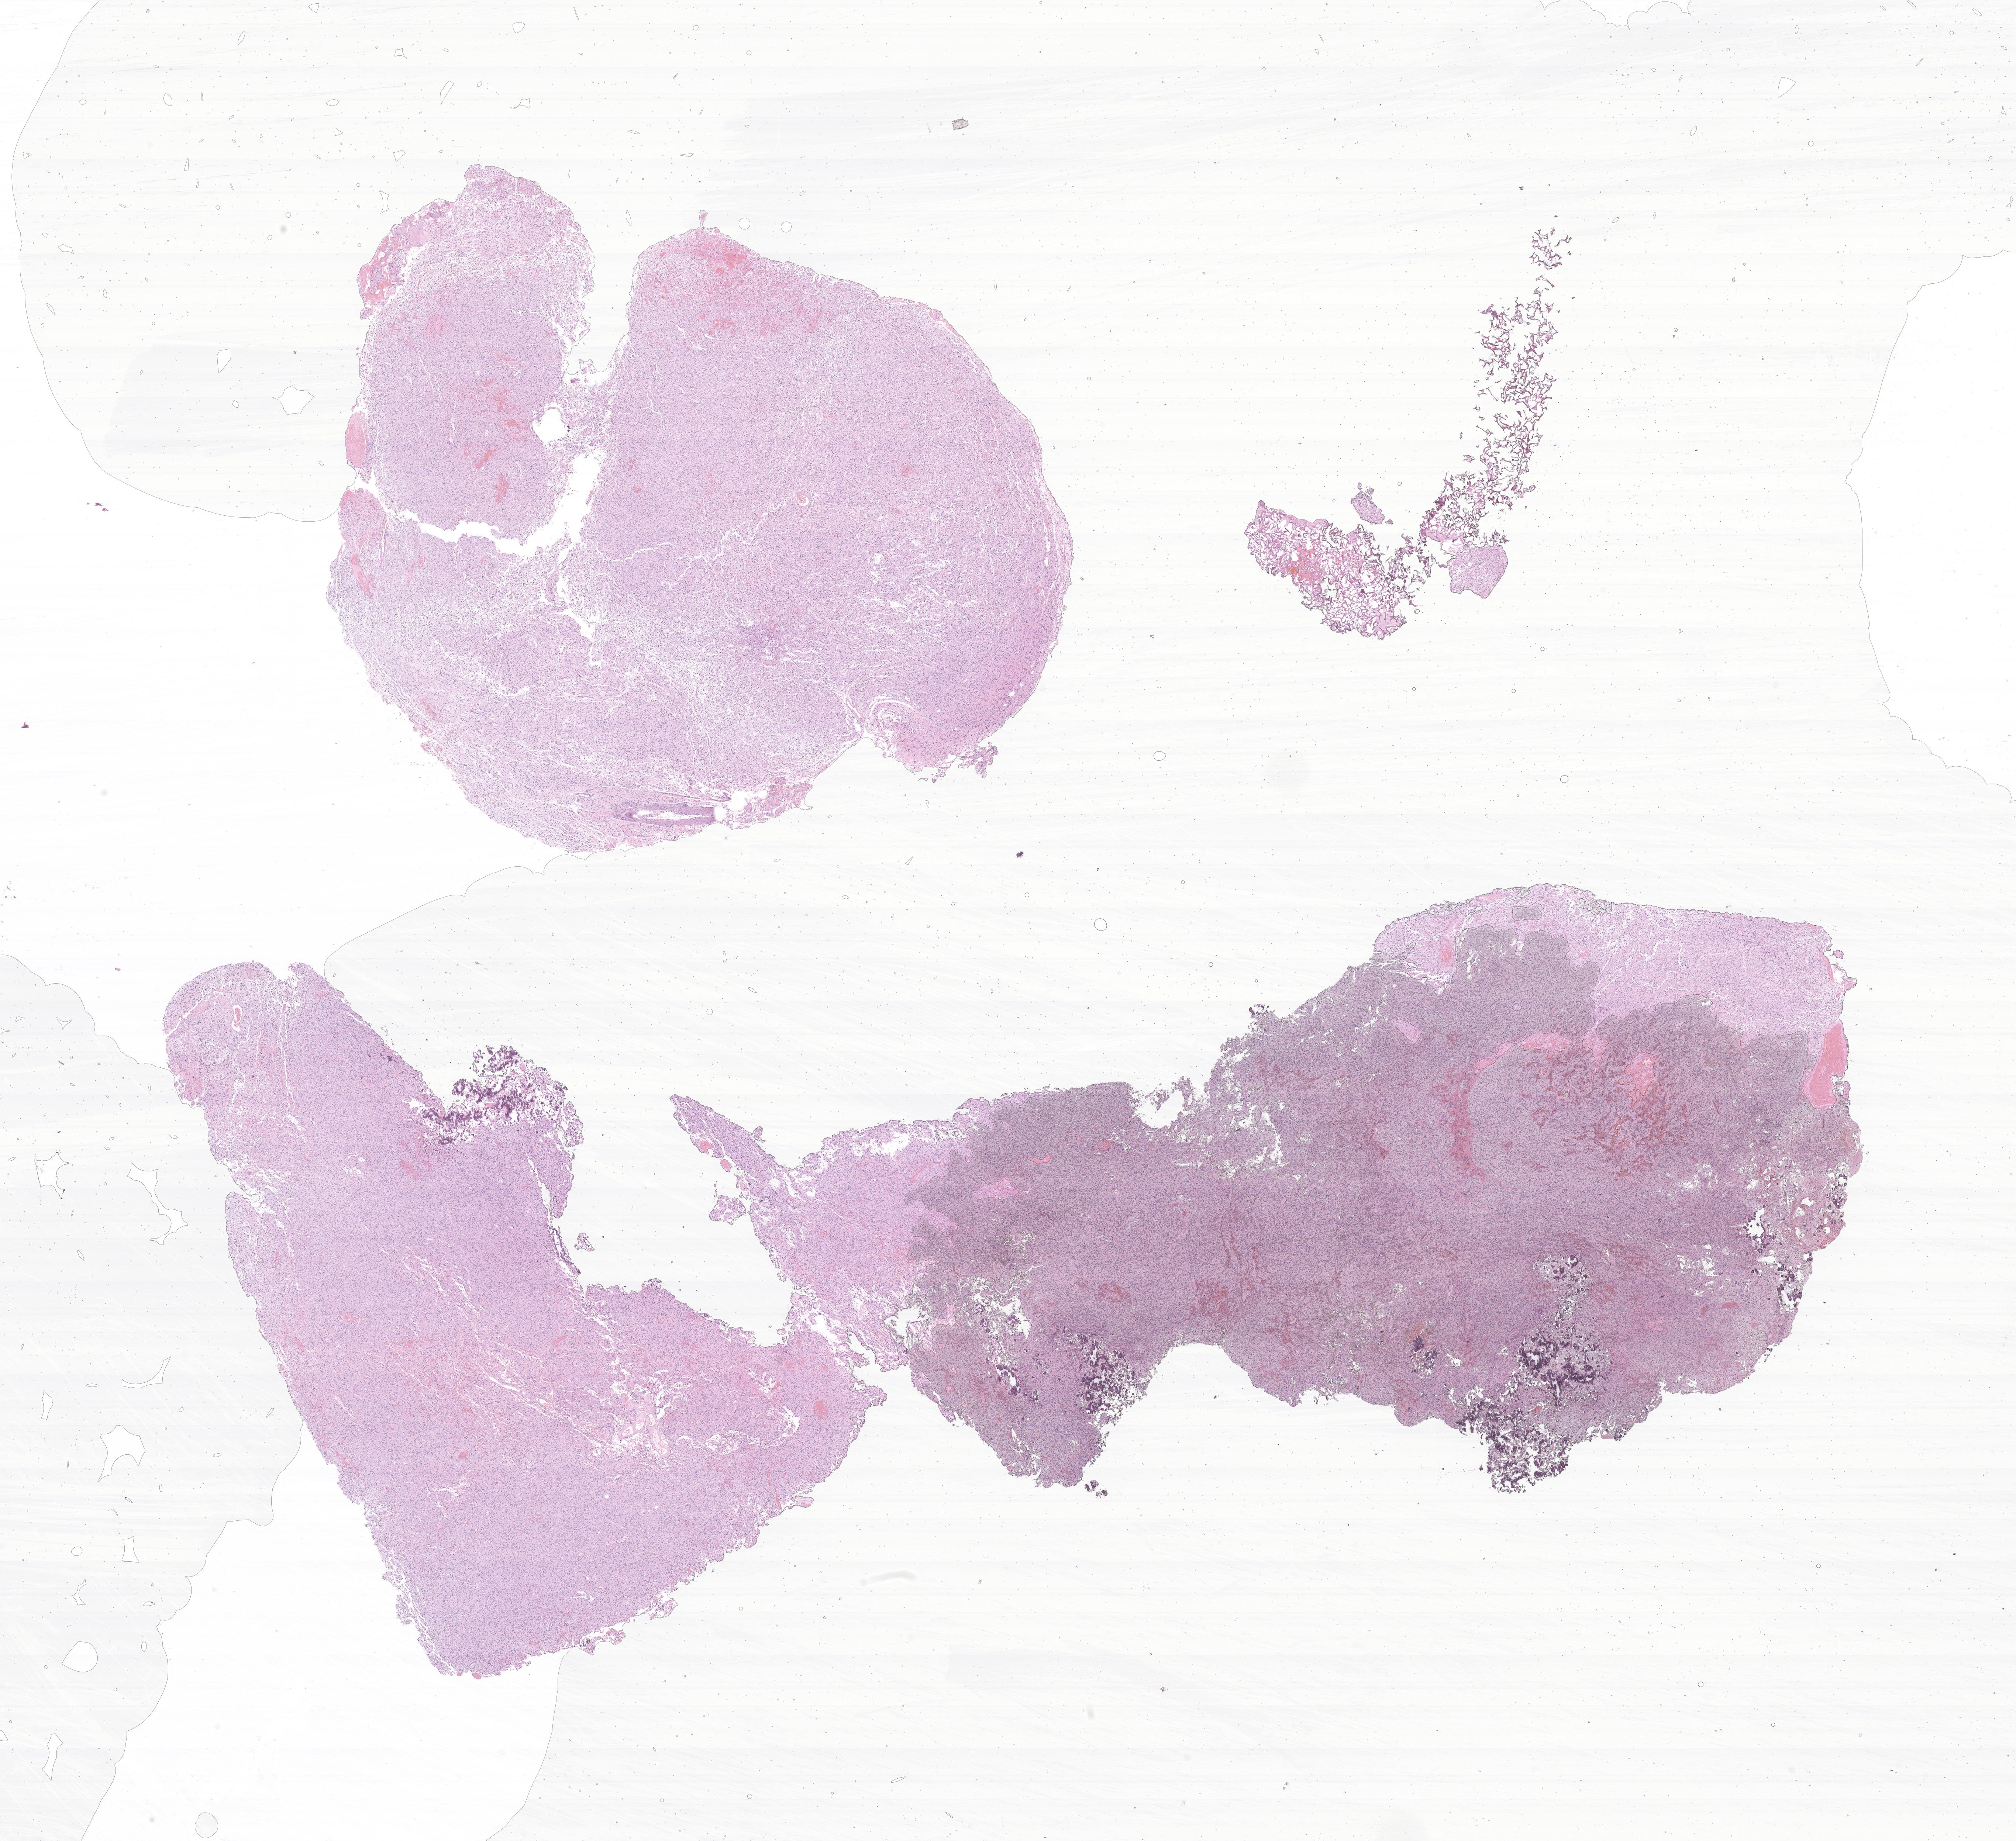
H&E whole-slide image of tumor tissue from the brain, a low-resolution overview of the entire scanned area, about 23.0 x 21.0 mm. Formalin-fixed, paraffin-embedded (FFPE) tissue. Patient female; age 193 months (16 years 1 month).
Diagnosis: Pilocytic astrocytoma.